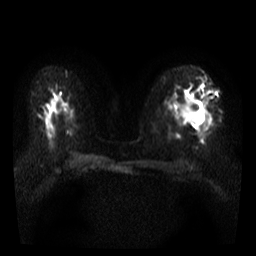
Breast MRI, one axial slice. Position 19 of 36 along the scan axis. Diffusion-weighted series; image 2 of 4 stored at this slice position (different b-values; order by instance number). 3 T. 256 × 256 image matrix, field of view 300 × 300 mm. Female patient.
Annotated regions visible in this slice (manually delineated by an expert):
- tumour on diffusion-weighted imaging: bounding box <191,113,203,126> (left, top, right, bottom; pixels)